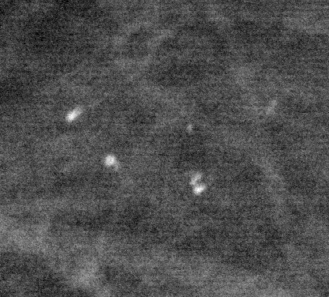
Cropped region of a digitized screen-film mammogram centred on a radiologist-marked abnormality; right breast; MLO view.
- Calcifications, morphology punctate, distribution clustered; BI-RADS assessment category 4; subtlety rating 5 on a 1 (subtle) to 5 (obvious) scale; pathology result (as recorded, not read from the image): benign.